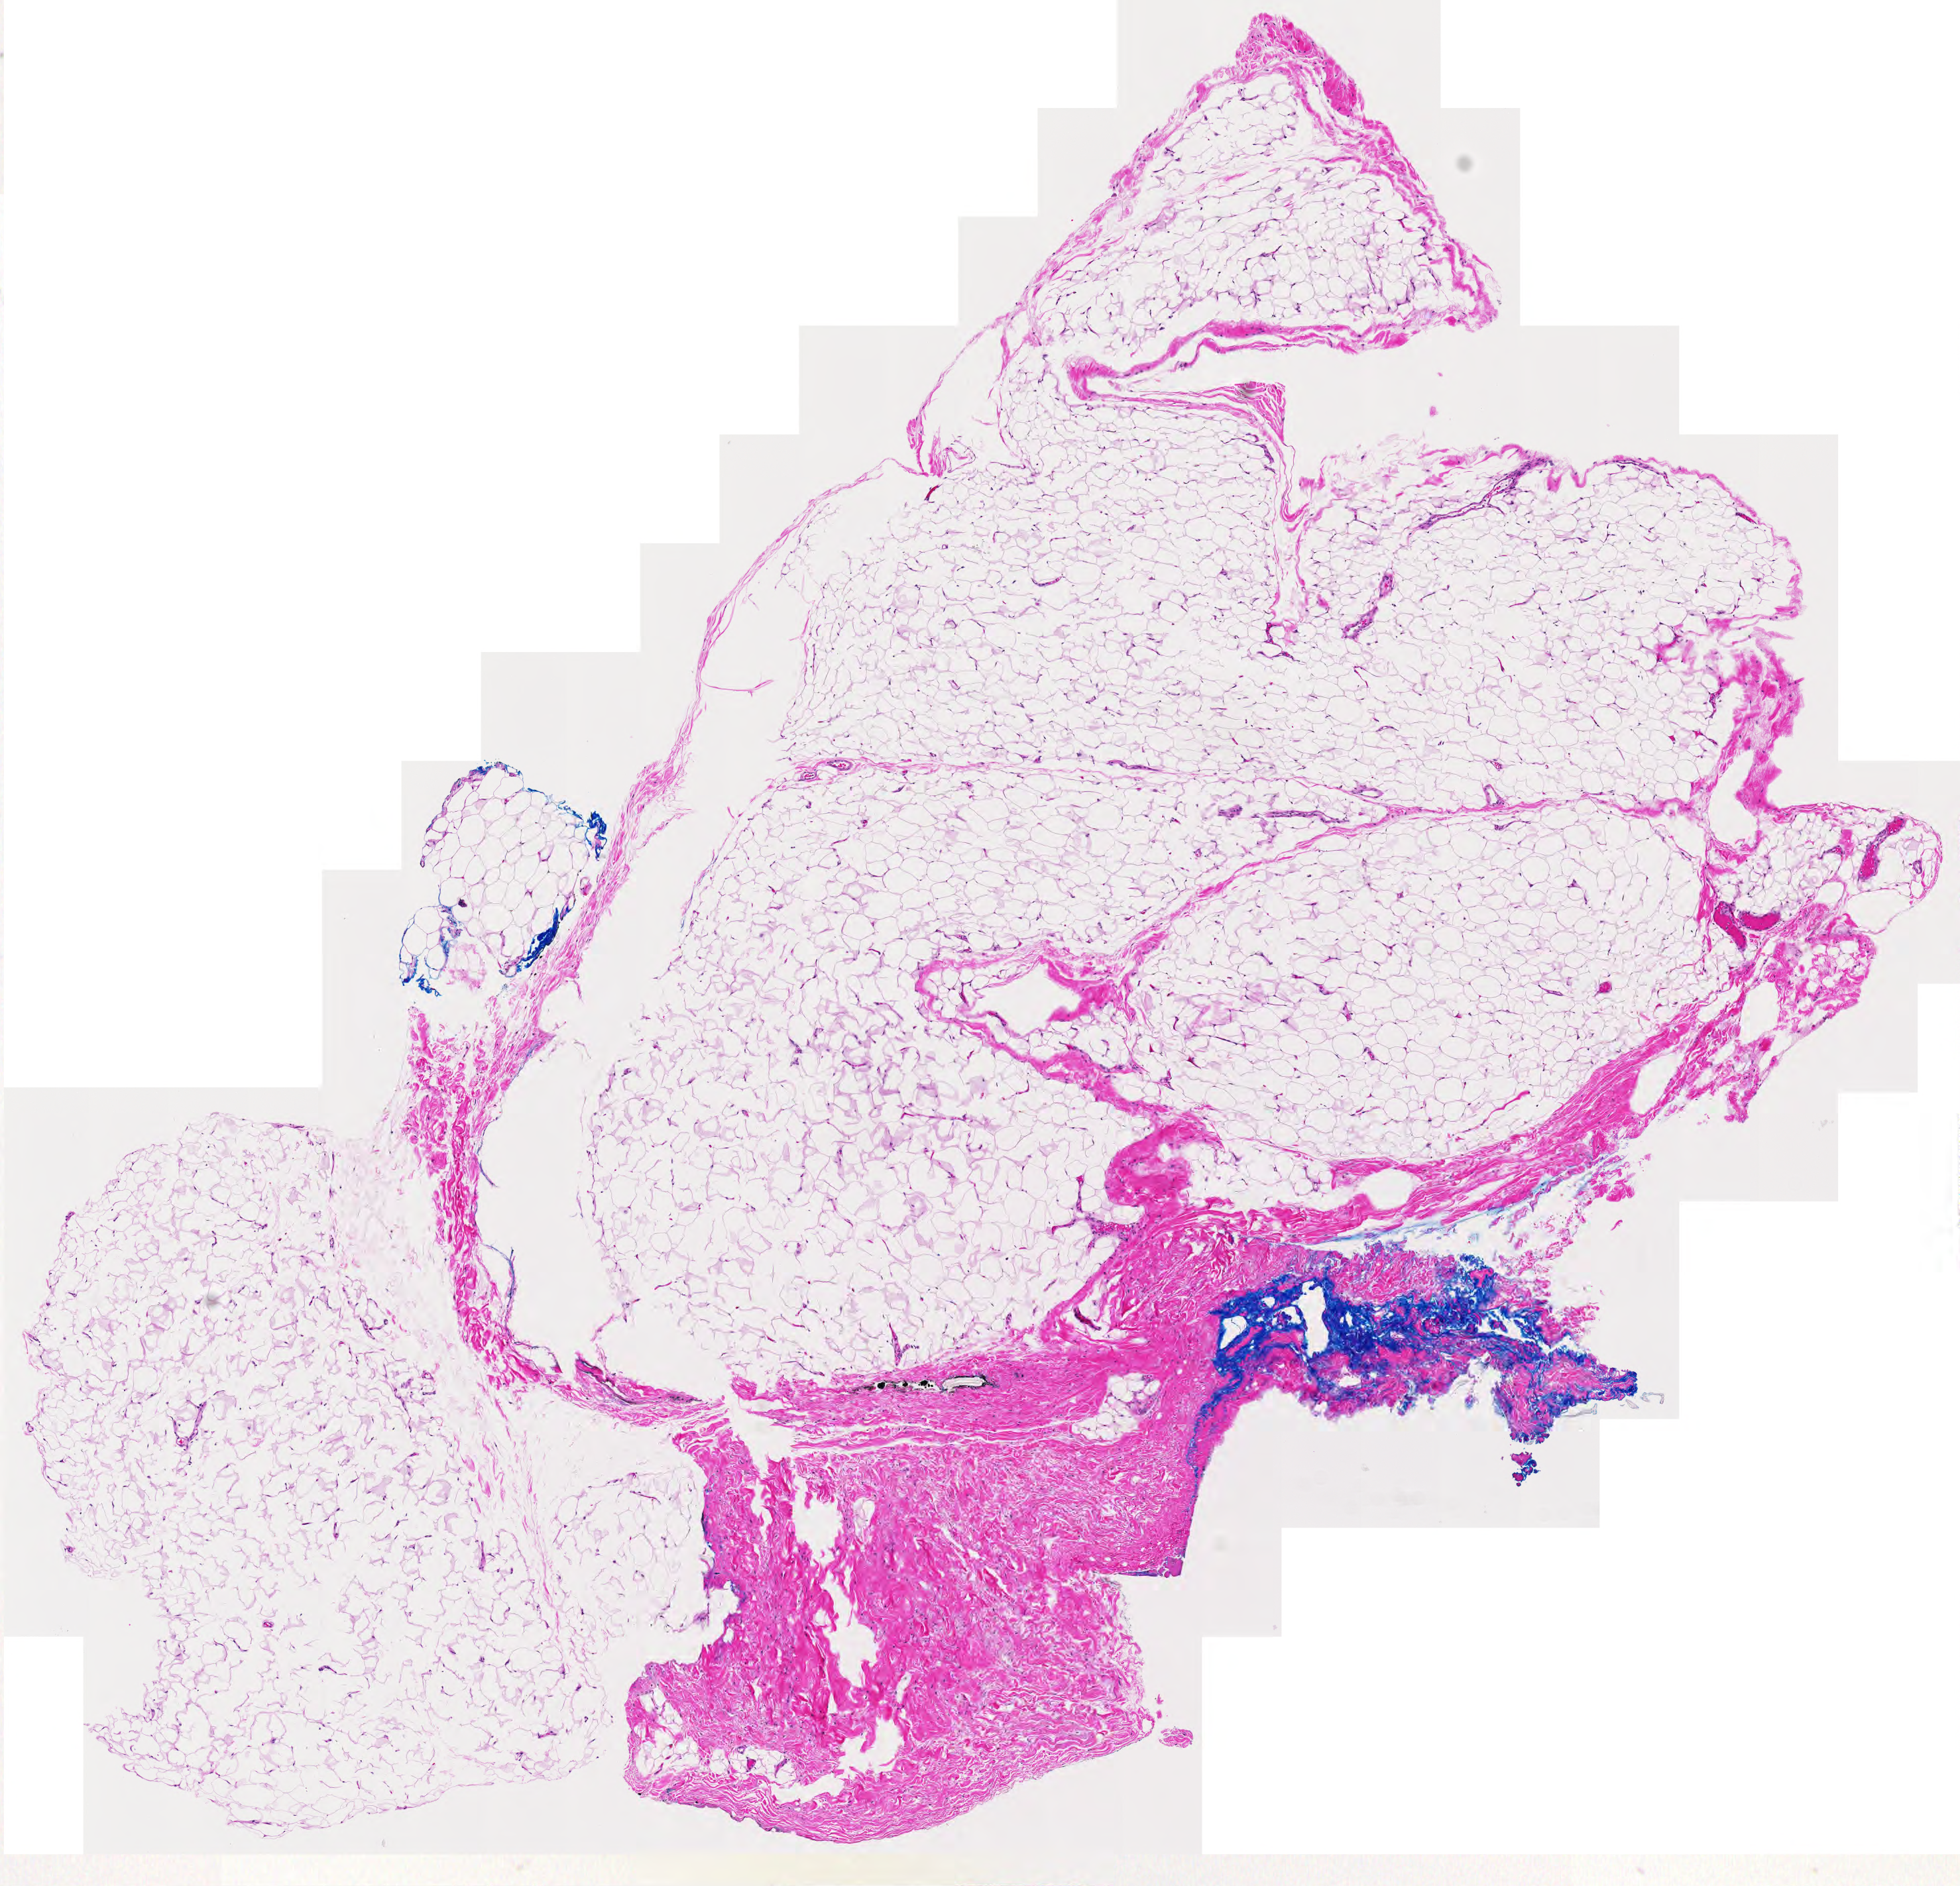
Hematoxylin and eosin (H&E) stained whole-slide image, a low-resolution overview of the entire scanned area, about 7.6 x 7.3 mm (acquisition: 20x scan), normal (non-tumour) tissue sample. Female, 41 y/o.
- this section: normal (non-tumour) tissue from the same patient
- patient diagnosis (cohort enrolment): sarcoma (site not recorded at cohort level)